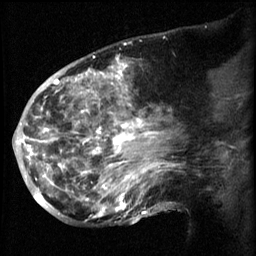
Breast MRI (dynamic contrast-enhanced), one sagittal slice; position 29 of 60 along the scan axis; 3 images stored at this slice position (order not interpretable as contrast timing); 1.5 T; TE 4.2 ms, TR 8.2 ms; 2.3 mm slice thickness; 256 × 256 image matrix, field of view 200 × 200 mm. Female patient, age 50 years.
Annotated regions visible in this slice (semi-automatically segmented with operator editing):
- analysis volume of interest (the breast-tissue region the enhancement analysis was run in; not a lesion): bounding box (x1, y1, x2, y2) in pixels: (50, 64, 169, 217)
- tumour enhancement mask (voxels above the 70 % enhancement threshold inside the analysis volume of interest): (50, 64, 161, 217)